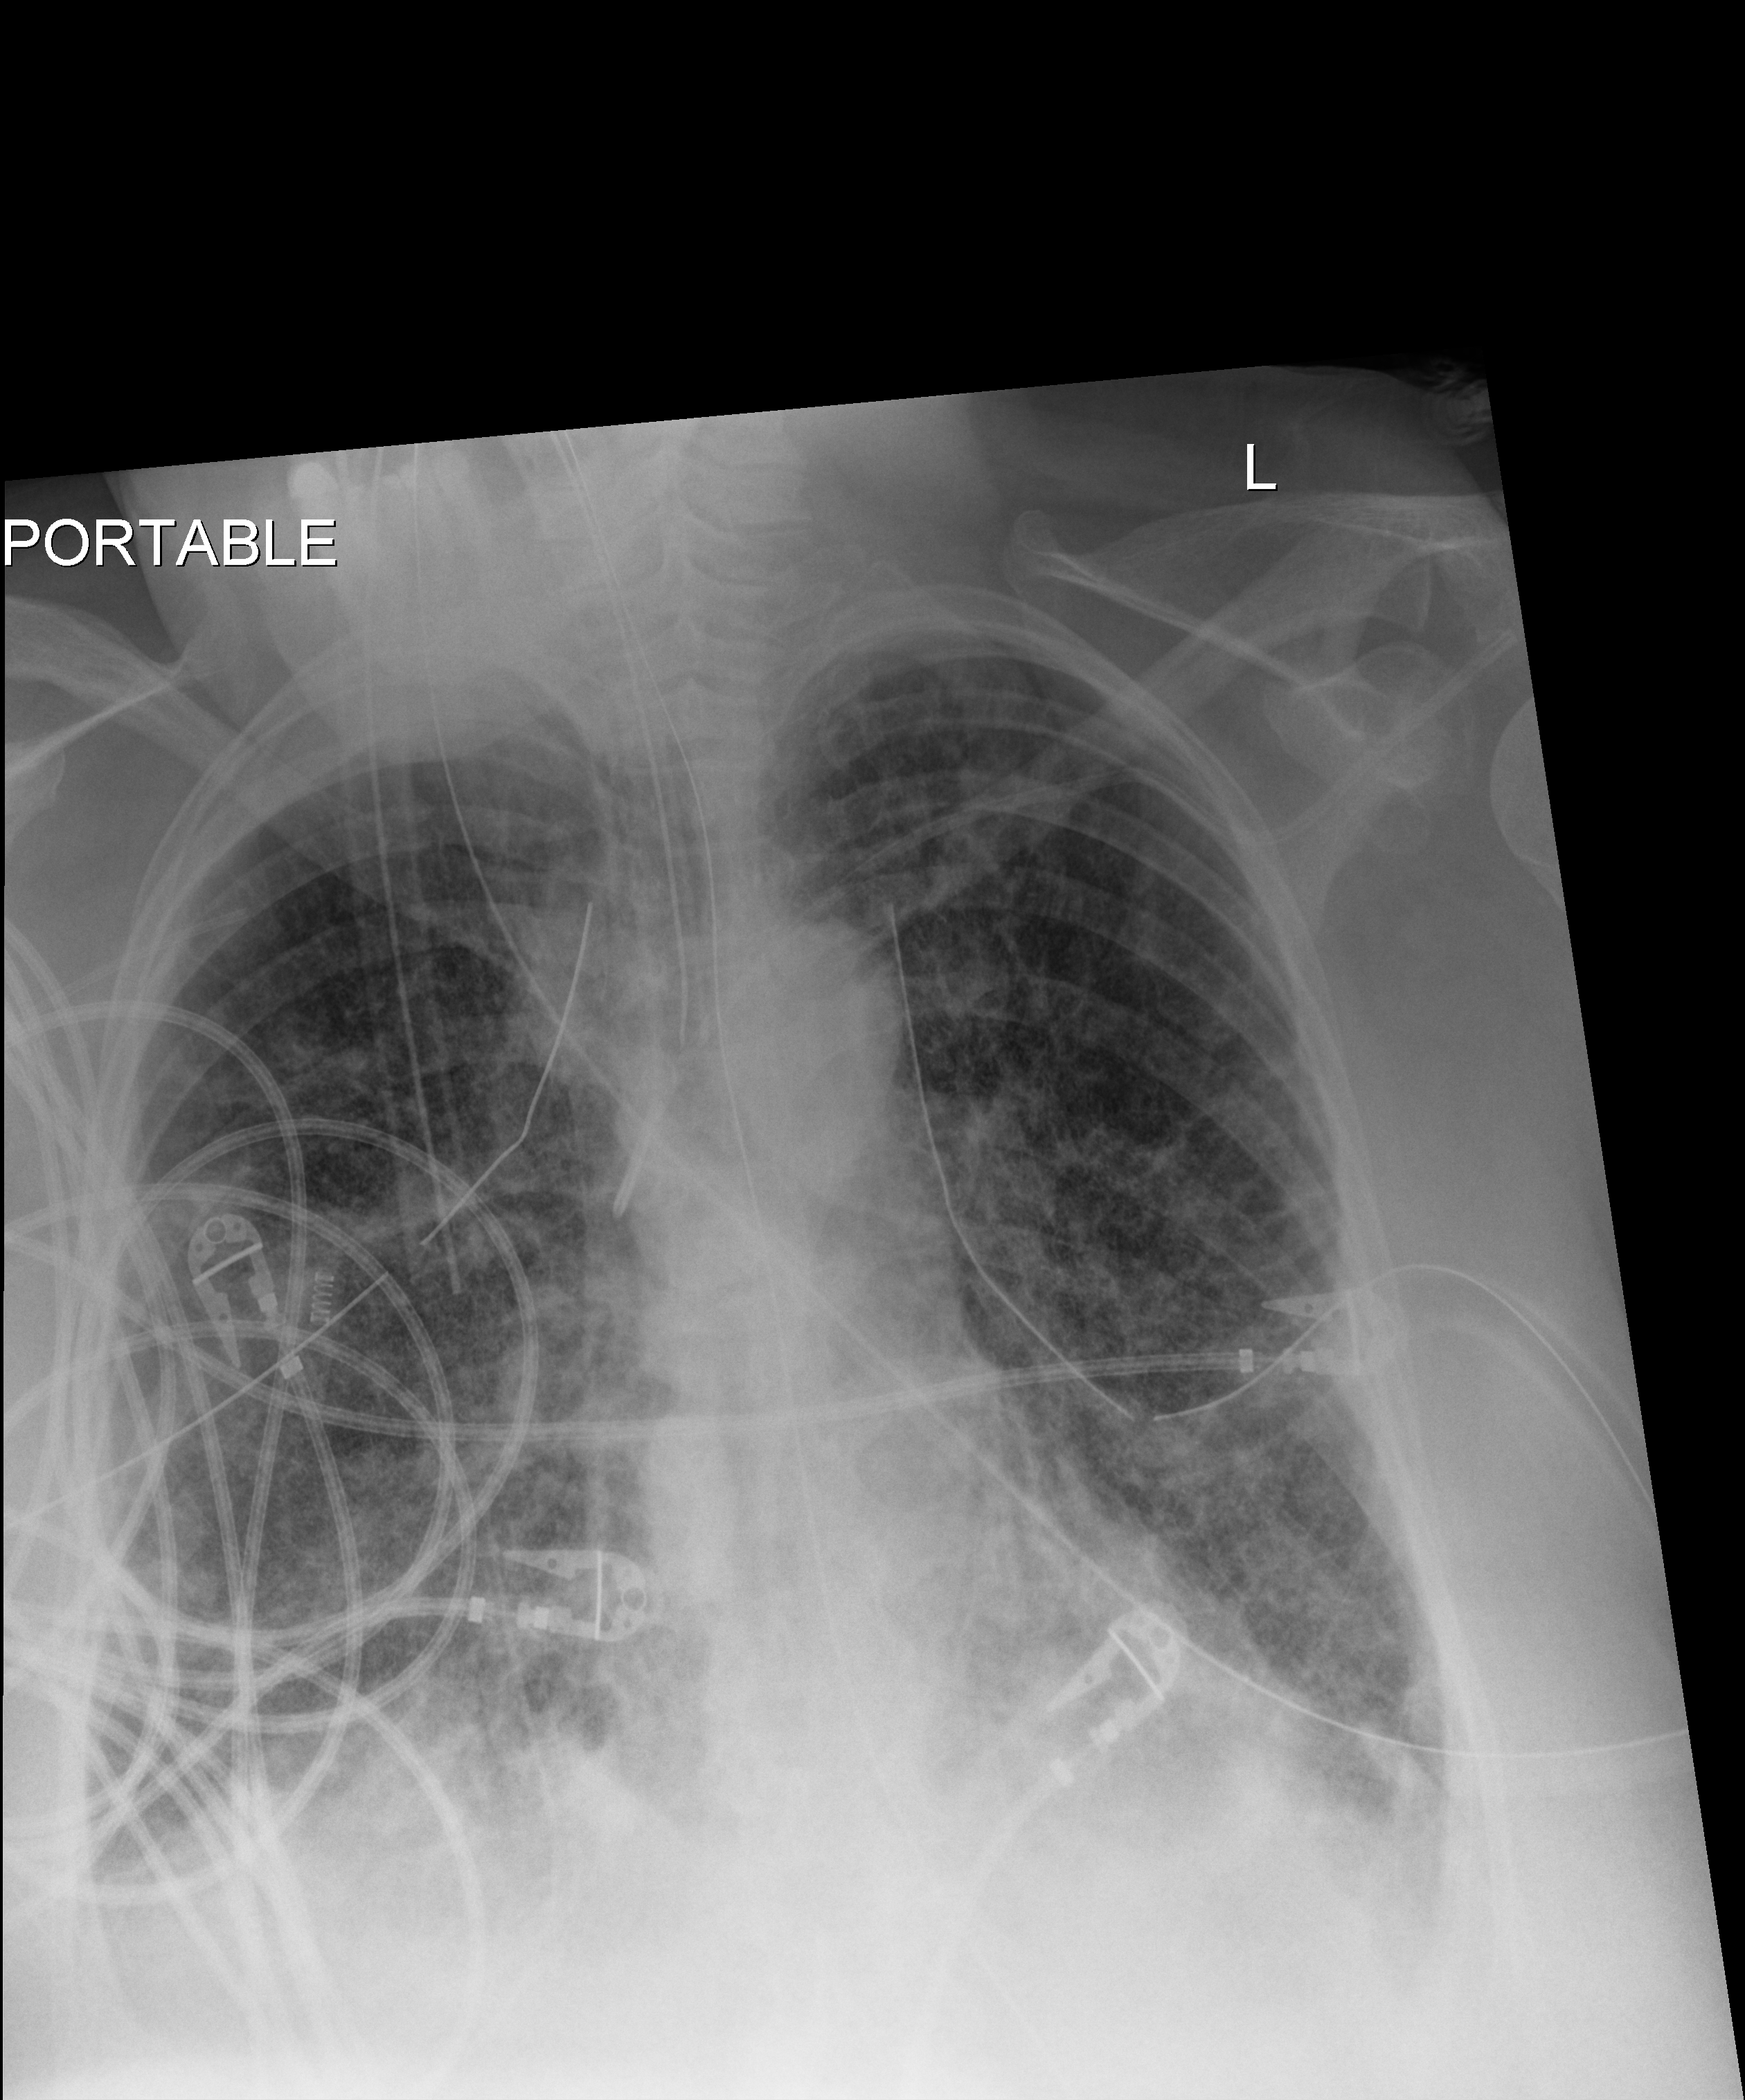
Portable chest radiograph, anteroposterior (AP) projection. Female patient hospitalised with COVID-19, age 60–74 years.
Admission-level facts for this patient (not findings on this image; timing relative to this image not recorded):
- mechanically ventilated during this hospital stay: yes
- other chronic lung disease (admission record): no
- diabetes (admission record): no